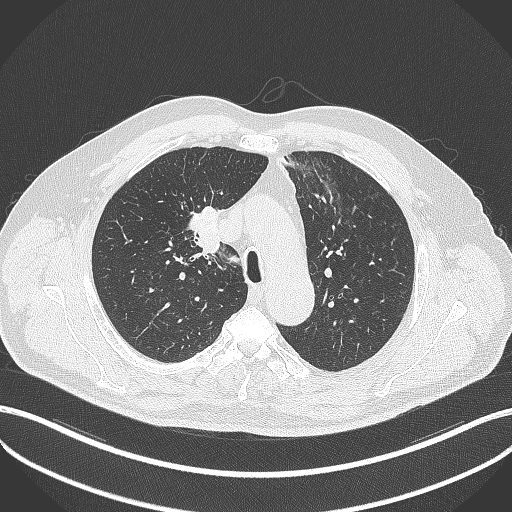
Chest CT, one axial slice; position 284 of 411 along the scan axis; reconstruction kernel B70f; lung window (W 1500 / L -600 HU); 1 mm slice thickness; 512 × 512 image matrix, field of view 400 × 400 mm. Patient: male, 60 years. Case-level facts recorded for this patient, not image findings: clinical TNM (as recorded): T1b N1 M0.
Structures marked on this image (bounding box drawn by a radiologist):
- lung tumour (recorded histology: squamous cell carcinoma): bounding box (x1, y1, x2, y2) in pixels: (186, 201, 220, 259)